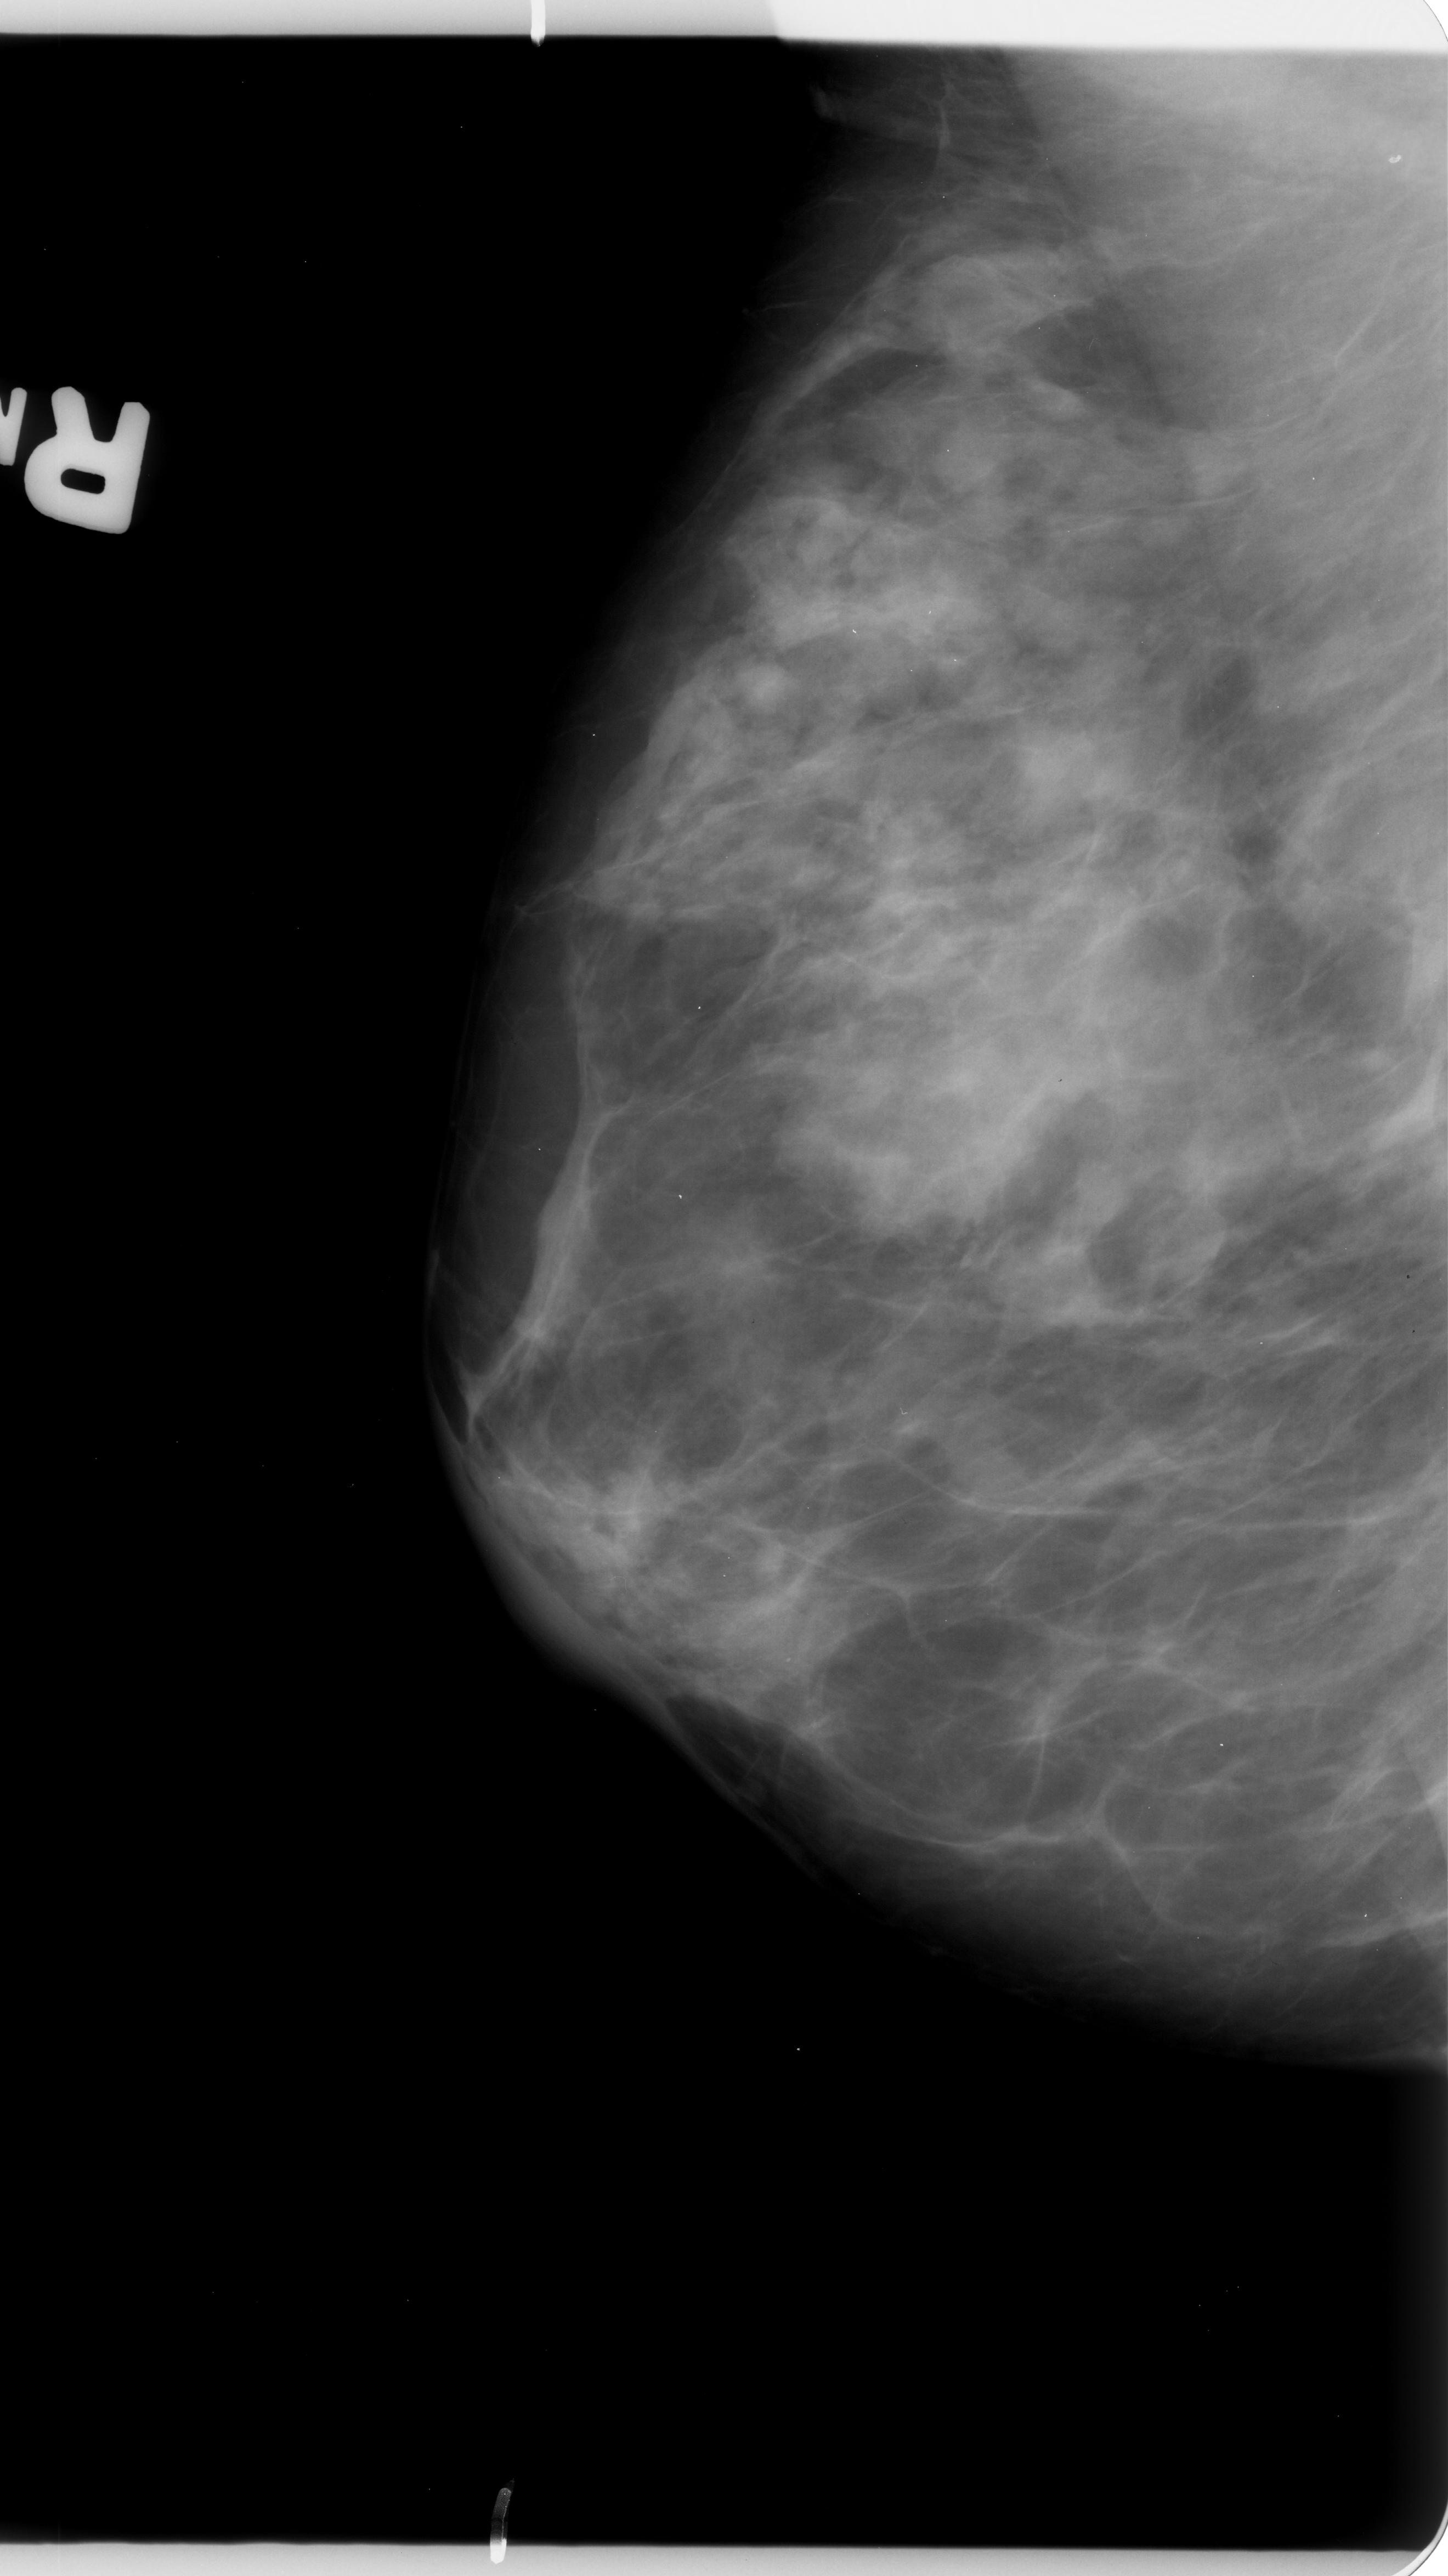
Digitized screen-film mammogram, right breast, mediolateral oblique (MLO) view, BI-RADS breast density category 3 (scale 1–4).
- Marked abnormality: mass, shape irregular / focal asymmetric density, margins ill defined; BI-RADS assessment category 3; pathology result (as recorded, not read from the image): benign.